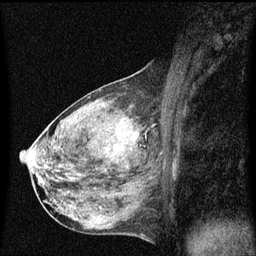
Breast MRI (dynamic contrast-enhanced), one sagittal slice. Slice 29 of 60 in the series (ordered by position). Dynamic contrast-enhanced series, image 2 of 3 at this slice position (ordered by acquisition). 1.5 T. TE 4.2 ms, TR 8 ms. 256 × 256 image matrix. Patient: female, 50 years.
Structures marked on this image (semi-automatically segmented with operator editing):
- analysis volume of interest (the breast-tissue region the enhancement analysis was run in; not a lesion): bounding box (x1, y1, x2, y2) in pixels: (106, 118, 147, 159)
- tumour enhancement mask (voxels above the 70 % enhancement threshold inside the analysis volume of interest): (133, 132, 138, 139)